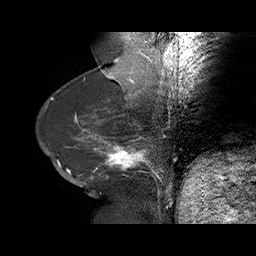
Breast MRI (dynamic contrast-enhanced), one sagittal slice. Slice 24 of 75 in the series (ordered by position). Dynamic contrast-enhanced series, time point 2 of 6 at this slice position (early post-contrast). 1.5 T. TE 4.5 ms, TR 32.4 ms. 256 × 256 image matrix. Female patient. From the clinical record (not read from this slice): setting: breast cancer imaged before/during neoadjuvant chemotherapy; receptor status: HR-positive, HER2-negative.
Annotated regions visible in this slice (semi-automatically segmented with operator editing):
- analysis volume of interest (the breast-tissue region the enhancement analysis was run in; not a lesion): box from (x=58, y=134) to (x=166, y=191) px
- tumour enhancement mask (voxels above the 100 % enhancement threshold inside the analysis volume of interest): (x=66, y=137)–(x=161, y=177)